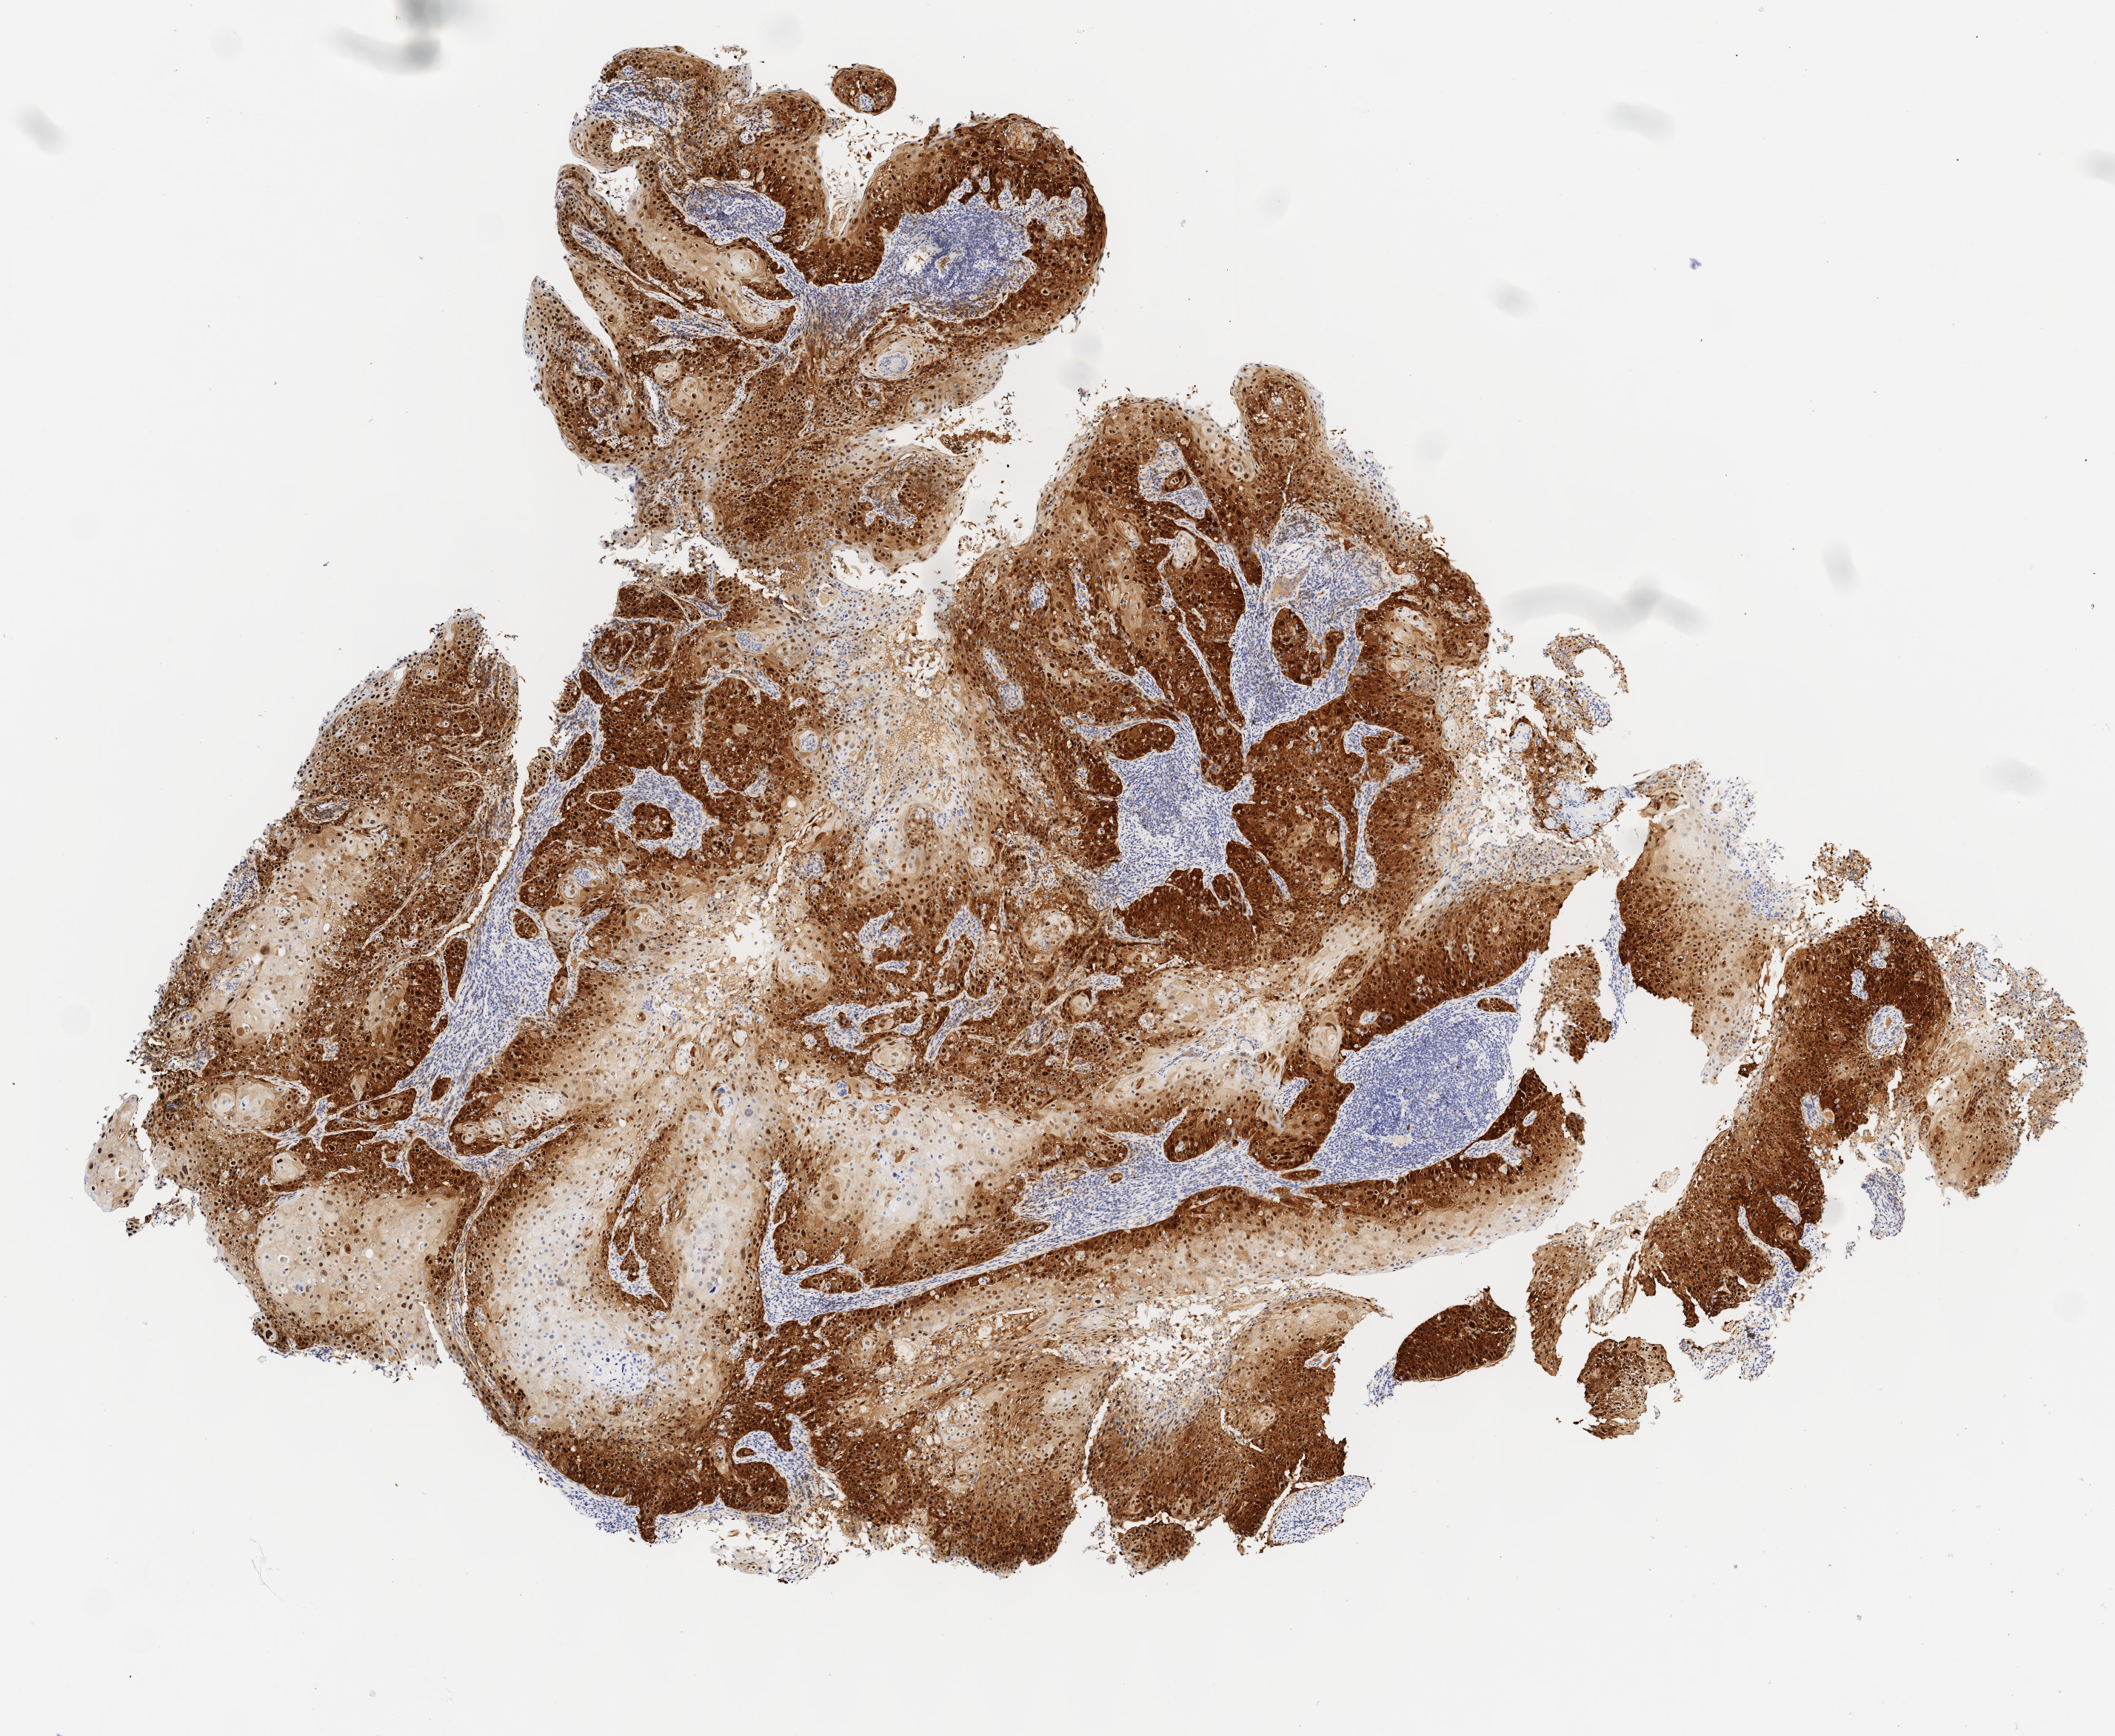
Immunohistochemistry (IHC) whole-slide image stained for p16 (p16INK4a), low-resolution overview of the scanned area, about 5.7 x 4.7 mm; specimen: tumor tissue; anatomic site: cervix. Patient female; age 31 years.
Histologic diagnosis: Squamous cell carcinoma, keratinizing, NOS.